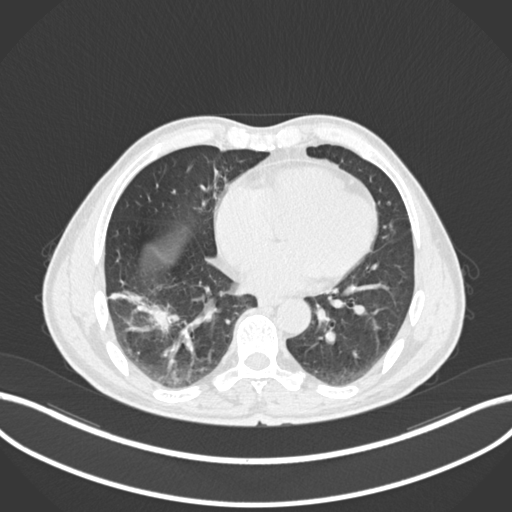
Chest CT, one axial slice; slice 61 of 208 in the series (ordered by position); 120 kVp; lung window (W 1500 / L -600 HU); 512 × 512 image matrix. Male patient, age 58 years. From the clinical record (not read from this slice): clinical TNM (as recorded): T3 N0 M0; histopathological grade: G2.
Outlined on this slice (bounding box drawn by a radiologist):
- lung tumour (recorded histology: squamous cell carcinoma): bounding box <112,284,187,334> (left, top, right, bottom; pixels)